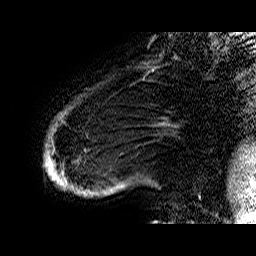
Breast MRI (dynamic contrast-enhanced), one sagittal slice. Position 6 of 60 along the scan axis. Dynamic contrast-enhanced series, time point 2 of 6 at this slice position (early post-contrast). 1.5 T. TE 6.4 ms, TR 32.9 ms. 4 mm slice thickness. 256 × 256 image matrix, field of view 200 × 200 mm. Female patient. From the clinical record (not read from this slice): setting: breast cancer imaged before/during neoadjuvant chemotherapy; receptor status: HR-positive, HER2-negative.
Structures marked on this image (semi-automatically segmented with operator editing):
- analysis volume of interest (the breast-tissue region the enhancement analysis was run in; not a lesion): bounding box (x1, y1, x2, y2) in pixels: (44, 87, 173, 205)
- tumour enhancement mask (voxels above the 100 % enhancement threshold inside the analysis volume of interest): (44, 152, 67, 185)